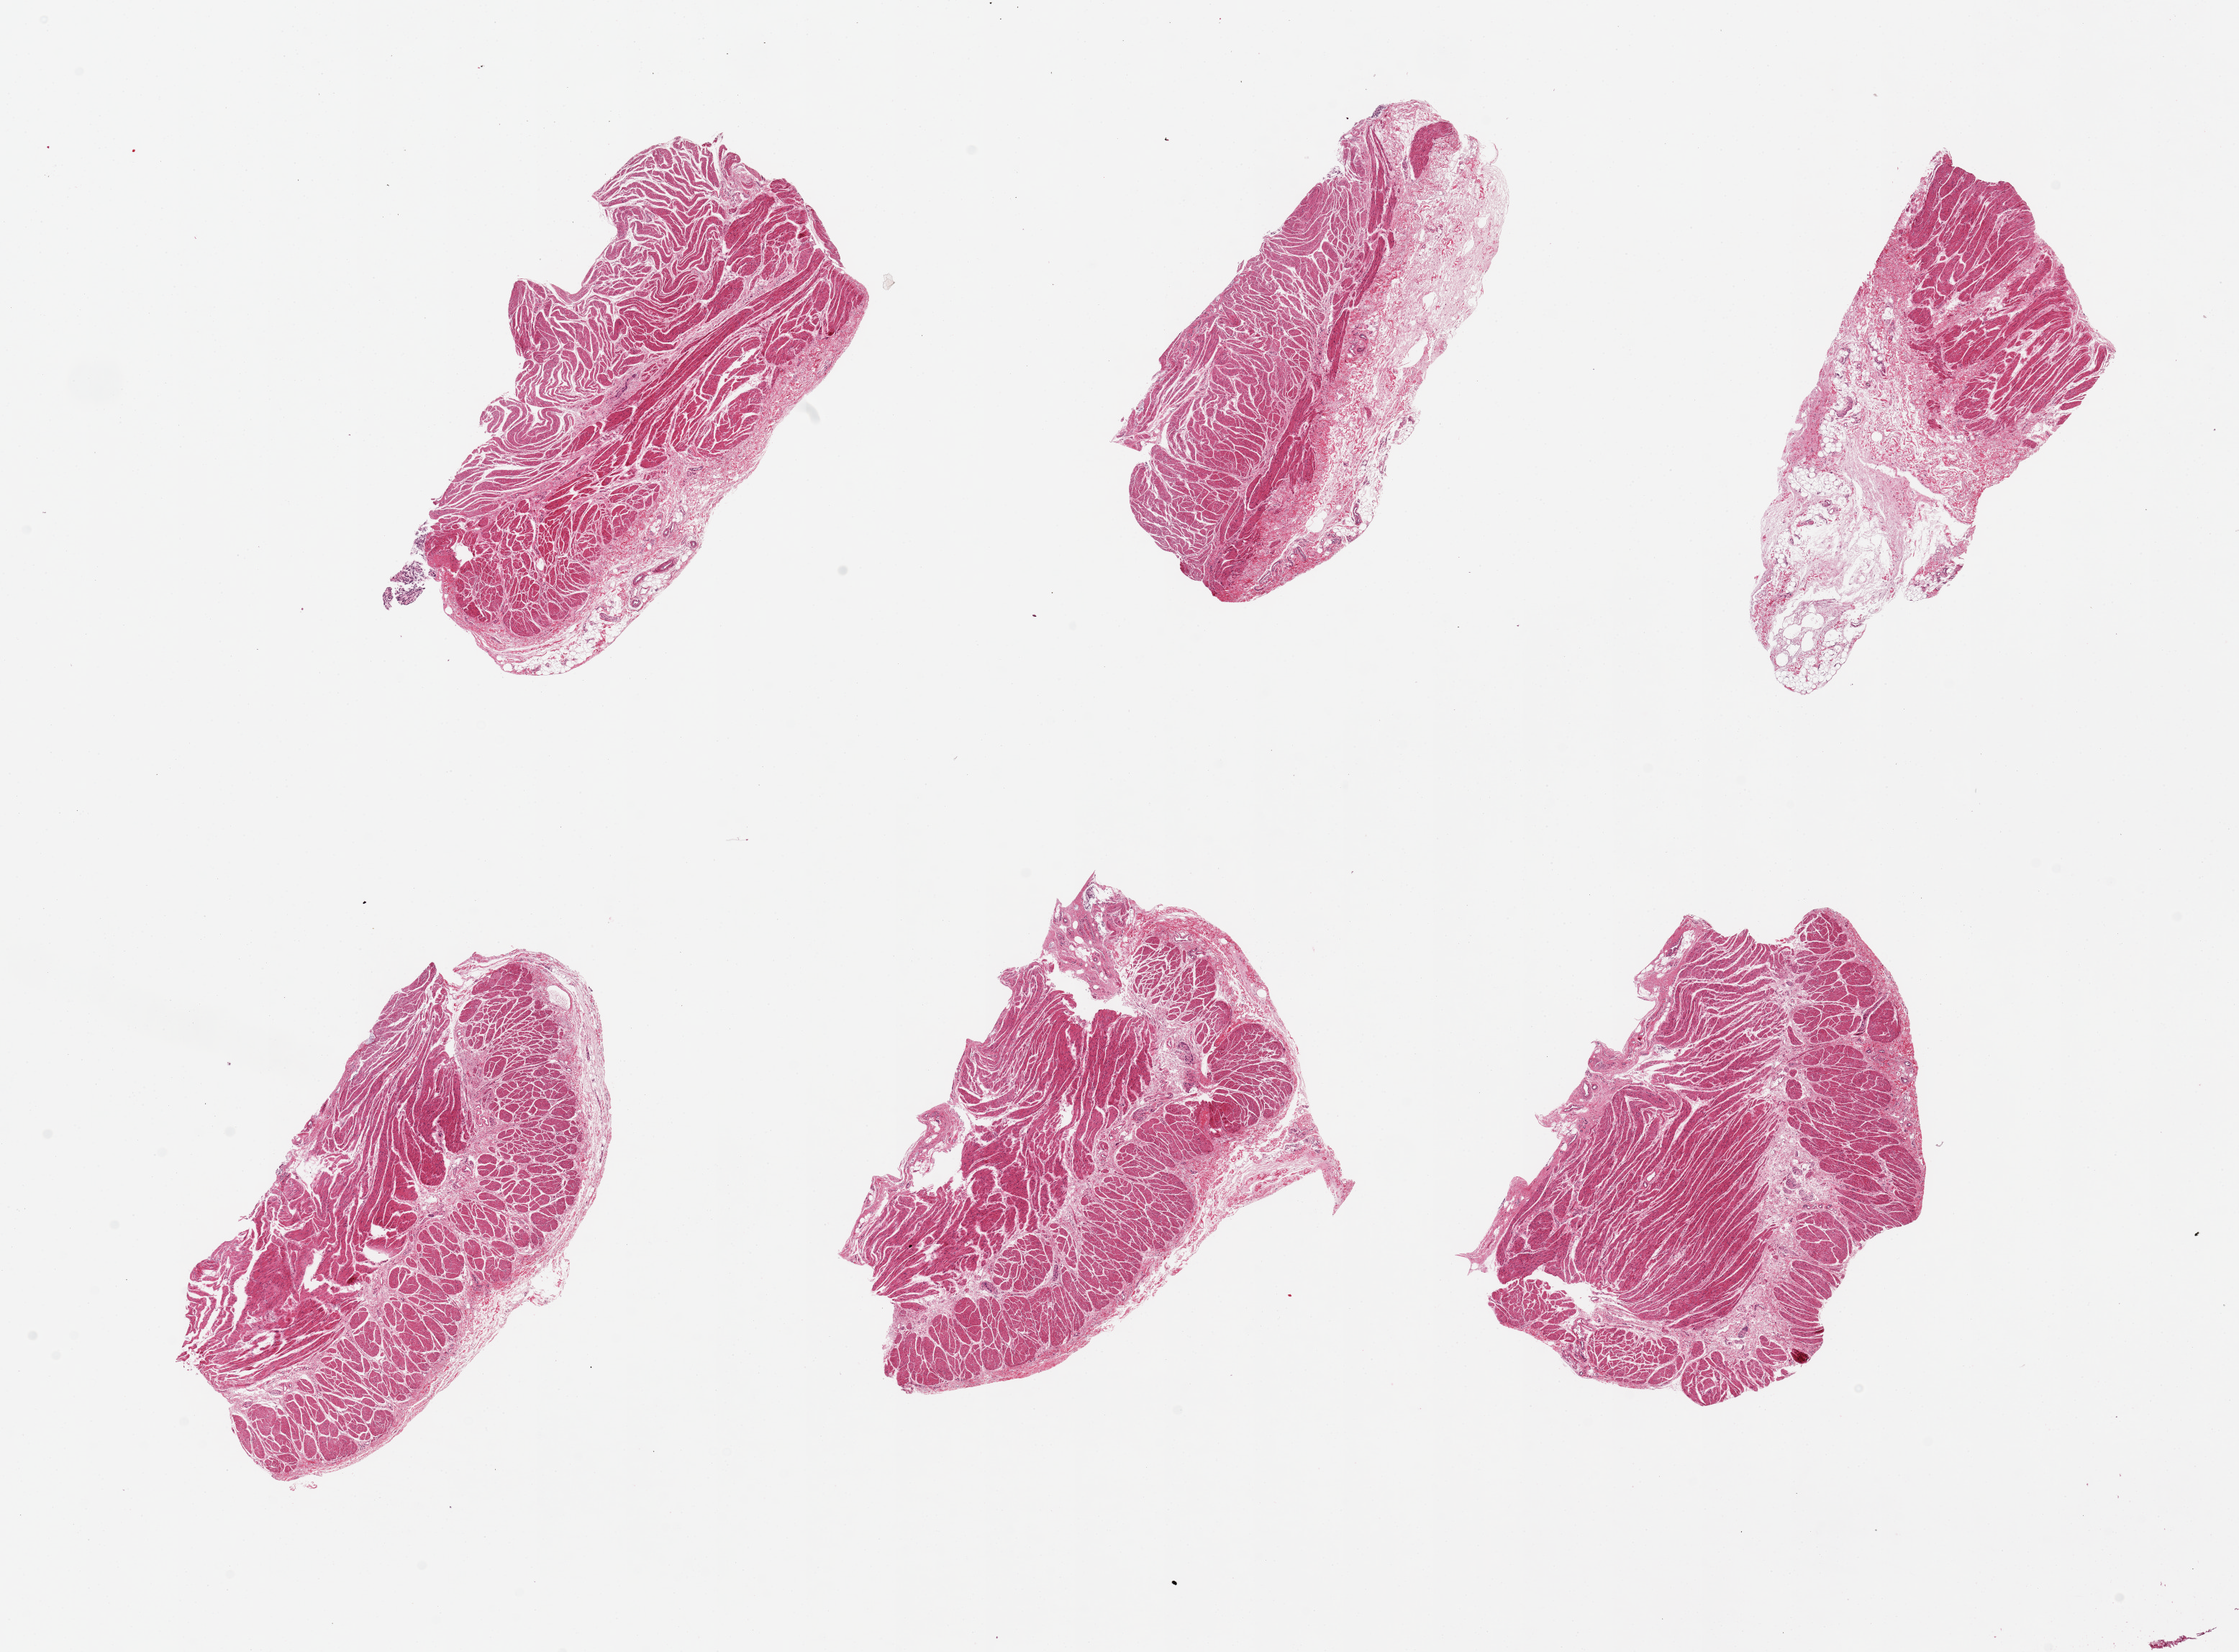
Whole-slide image, haematoxylin and eosin stain, whole scanned area (about 24.6 x 18.2 mm) shown as a low-resolution overview, PAXgene-fixed paraffin-embedded (PFPE) section, section of gastroesophageal junction (target tissue), donor tissue sample. Donor: male.
Review note (as recorded): 6 pieces, up to 6x3.5mm; 10, 30, & 60% periesophageal stroma in 3 pieces.